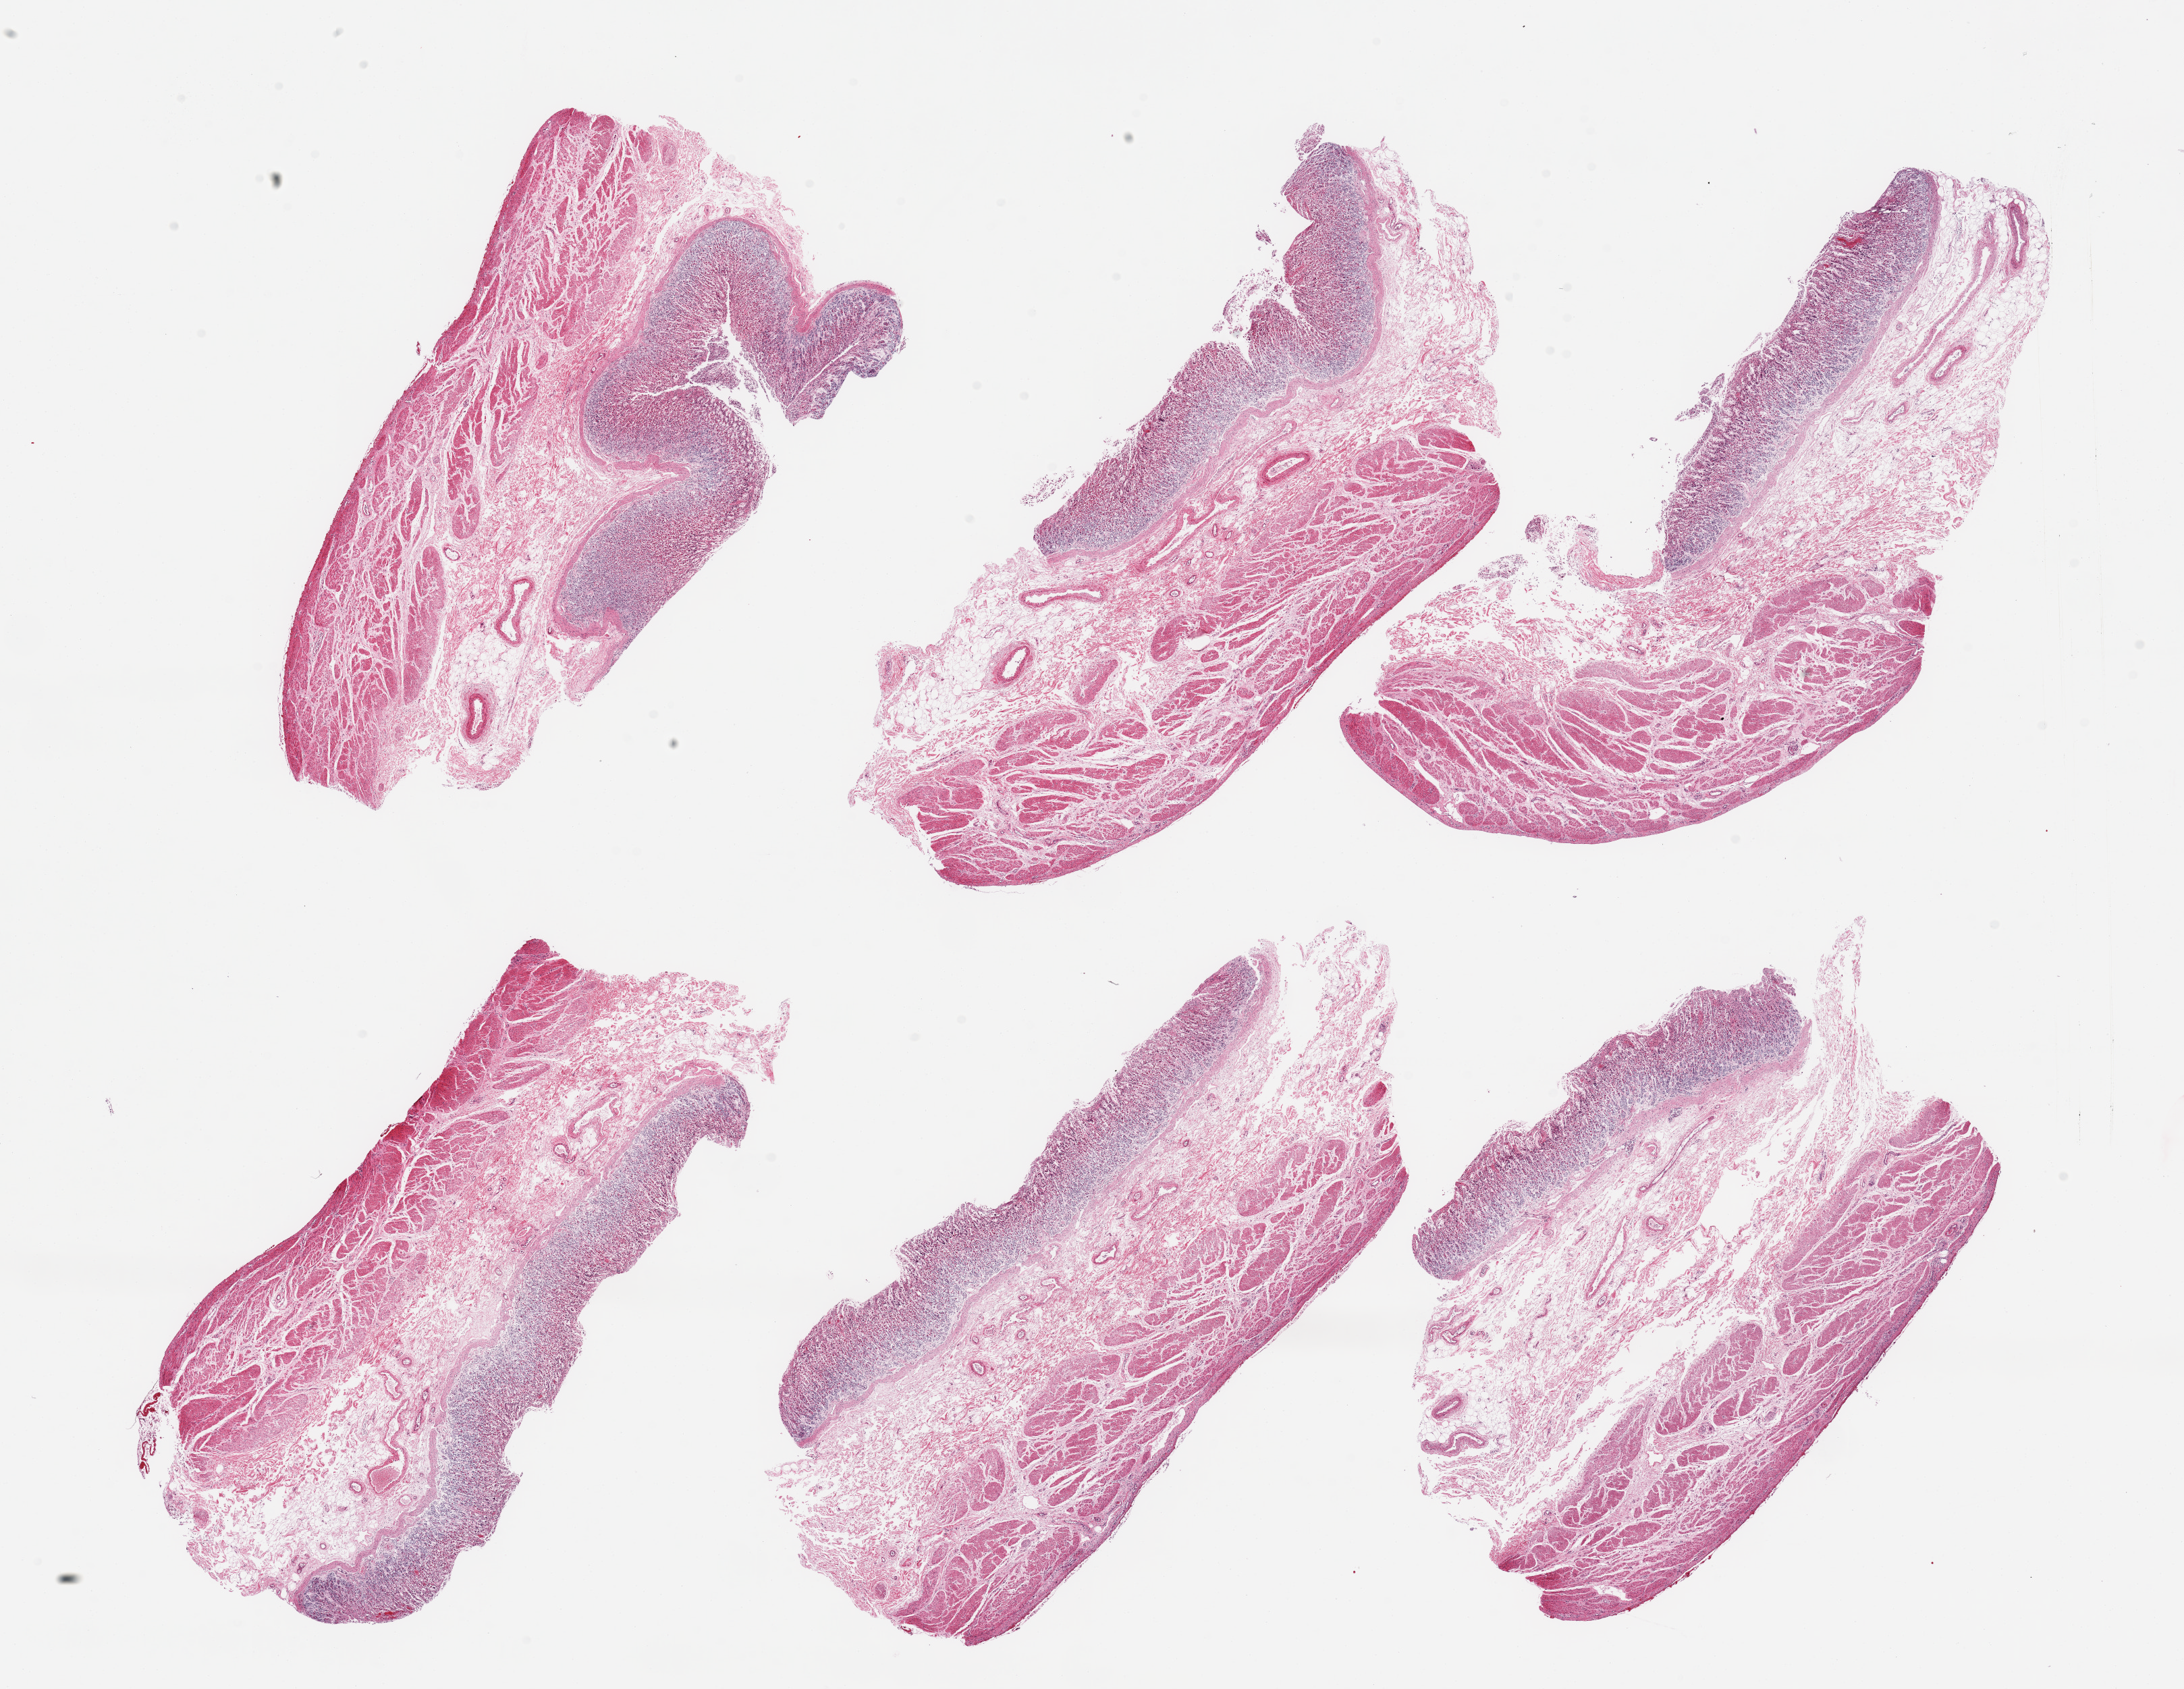
Haematoxylin and eosin whole-slide image, whole scanned area (about 25.6 x 19.8 mm, slide scanned at 20x) shown as a low-resolution overview. PAXgene-fixed paraffin-embedded (PFPE) section. Section of stomach (target tissue). Donor tissue sample. Donor sex: male.
Reviewer comment on this tissue sample: 6 pieces, target mucosa up to ~1mm but moderately-markely autolyzed.